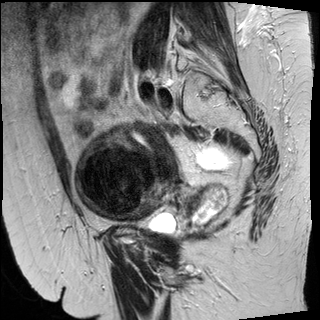
Pelvic MRI for cervical cancer, one sagittal slice. Position 19 of 50 along the scan axis. T2-weighted. 1.5 T. TE 89 ms, TR 4880 ms. 4 mm slice thickness. 320 × 320 image matrix, field of view 260 × 260 mm. Female patient, age 50 years.
Structures marked on this image (expert manual segmentation):
- uterus and cervix: bounding box (x1, y1, x2, y2) in pixels: (74, 122, 227, 234)